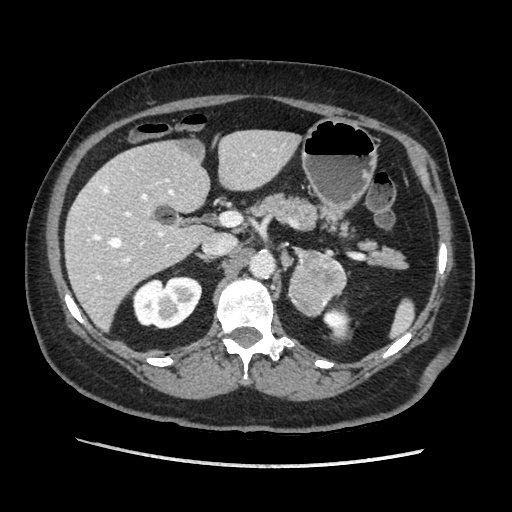
Contrast-enhanced abdominal CT, one axial slice; slice 118 of 203 in the series (ordered by position); soft-tissue window (W 400 / L 40 HU); 1.25 mm slice thickness; 512 × 512 image matrix. Female patient. Case-level facts recorded for this patient, not image findings: diagnosis: adrenocortical carcinoma; tumour side: left adrenal; tumour size at pathology: 6.5 cm; Ki-67 index: 22 %; stage (as recorded): 2.
Structures marked on this image (semi-automatic segmentation, software-assisted and operator-edited):
- mass: bounding box (x1, y1, x2, y2) in pixels: (289, 251, 348, 315)